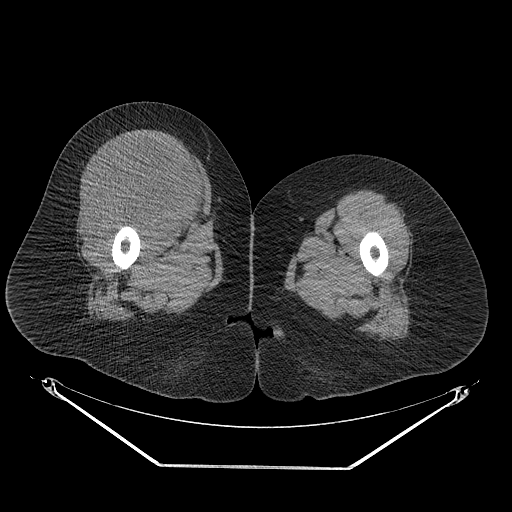
CT of an extremity soft-tissue mass (from a PET/CT study), one axial slice; slice 40 of 267 in the series (ordered by position); soft-tissue window (W 400 / L 40 HU); 3.75 mm slice thickness; 512 × 512 image matrix, field of view 500 × 500 mm. Female patient. Case-level facts recorded for this patient, not image findings: histological type: malignant solitary fibrous tumor; grade: intermediate; site of the primary tumour: right thigh.
Structures marked on this image (expert contour drawn on MRI and transferred to this co-registered scan by the dataset authors):
- gross tumour volume including surrounding oedema: bounding box (x1, y1, x2, y2) in pixels: (80, 137, 209, 234)
- gross tumour volume (mass): (87, 137, 204, 231)